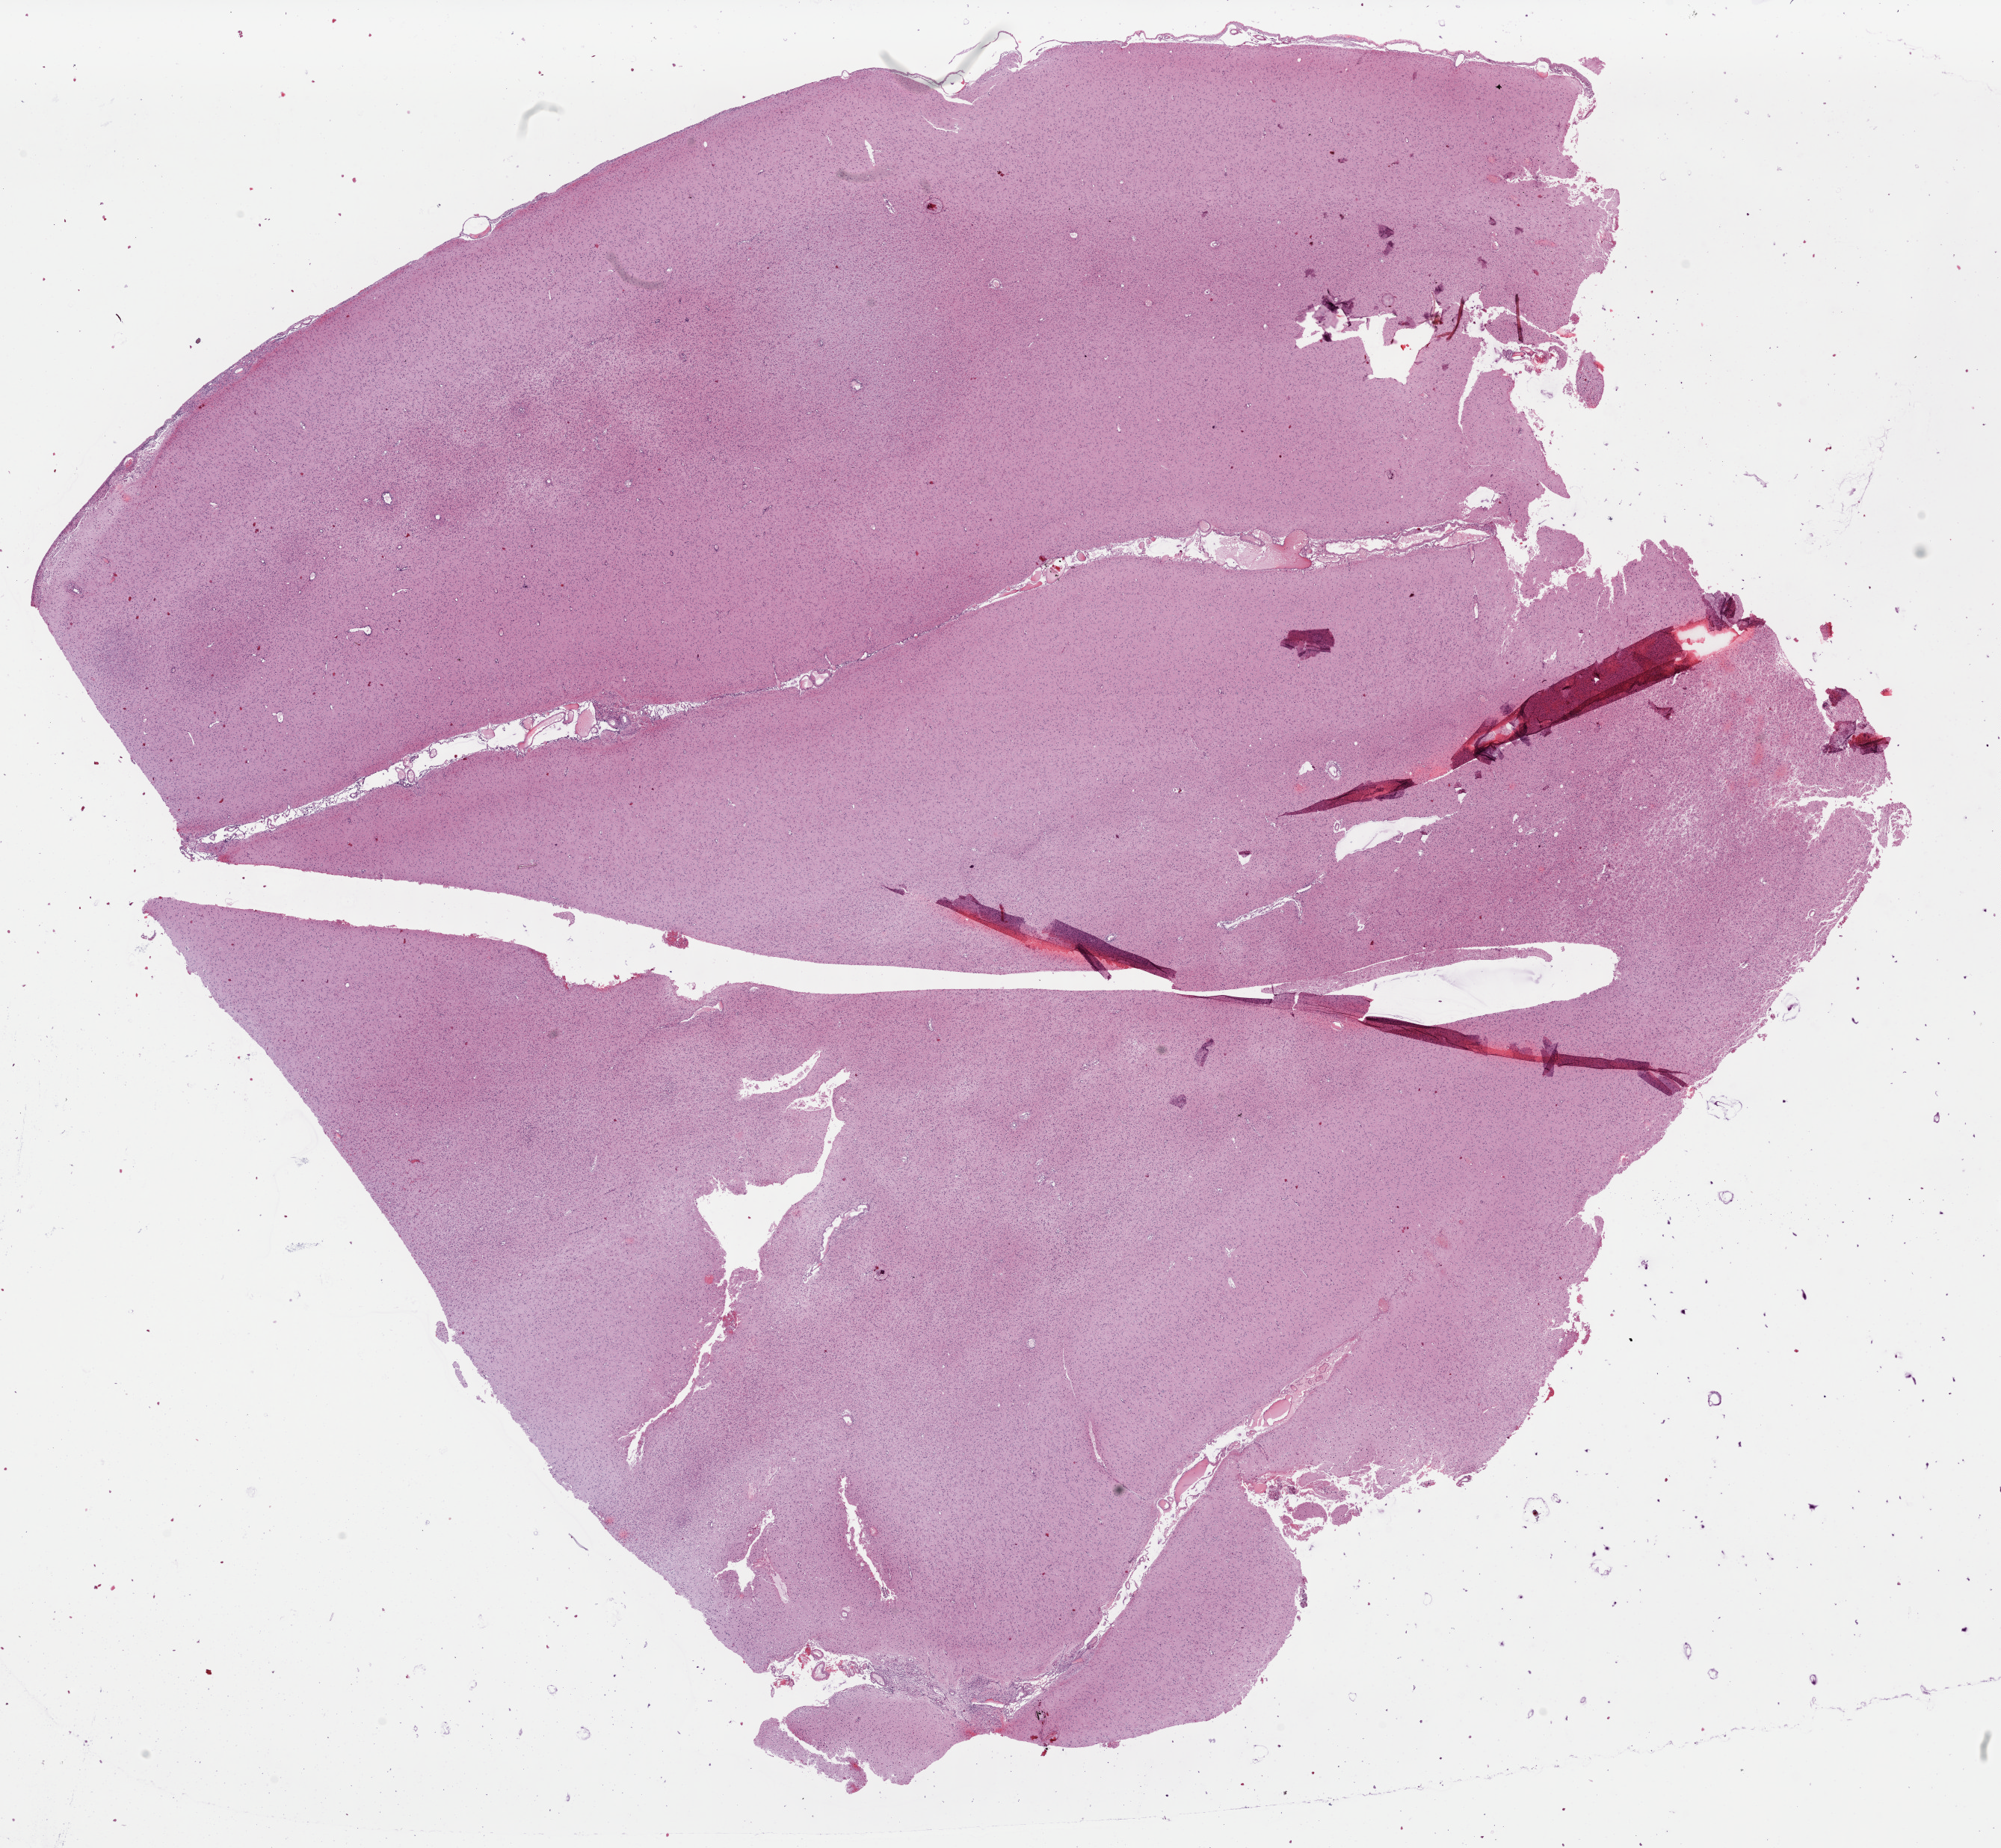
Digitized H&E-stained tissue section (whole slide) — whole scanned area (about 21.1 x 19.5 mm, slide scanned at 40x) shown as a low-resolution overview. FFPE section. Sample: primary tumour, brain. Patient: male, age at initial diagnosis 41 years. Histologic grade: G3 (poorly differentiated).
* histologic diagnosis: Astrocytoma, anaplastic (cerebrum)